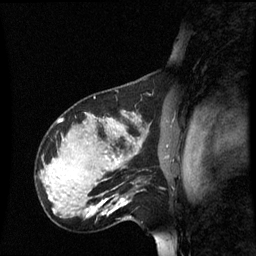
Breast MRI (dynamic contrast-enhanced), one sagittal slice. Position 44 of 60 along the scan axis. Dynamic contrast-enhanced series, image 2 of 3 at this slice position (ordered by acquisition). 1.5 T. TE 4.2 ms, TR 8.9 ms. 2.2 mm slice thickness. 256 × 256 image matrix, field of view 220 × 220 mm. Patient: female, 31 years. From the clinical record (not read from this slice): setting: breast cancer imaged before/during neoadjuvant chemotherapy; receptor status: HR-positive, HER2-negative.
Outlined on this slice (semi-automatic segmentation, software-assisted and operator-edited):
- analysis volume of interest (the breast-tissue region the enhancement analysis was run in; not a lesion): bounding box (x1, y1, x2, y2) in pixels: (90, 180, 134, 221)
- tumour enhancement mask (voxels above the 70 % enhancement threshold inside the analysis volume of interest): (90, 198, 128, 217)